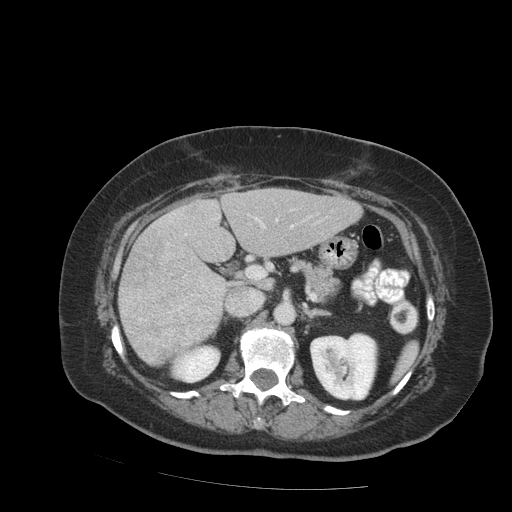
Contrast-enhanced abdominal CT (liver protocol), one axial slice. Slice 43 of 99 in the series (ordered by position). Soft-tissue window (W 400 / L 40 HU). 512 × 512 image matrix. Case-level facts recorded for this patient, not image findings: diagnosis: hepatocellular carcinoma (patient treated with transarterial chemoembolisation; whether this scan precedes or follows treatment is not stated here); TNM stage (as recorded): Stage-IVB; Child-Pugh class: A.
Structures marked on this image (semi-automatically segmented with operator editing):
- liver parenchyma outside the tumour (the mass and vessels are separate outlines, so this box may not span the whole liver): box from (x=118, y=188) to (x=362, y=364) px
- mass: (x=120, y=234)–(x=222, y=364)
- liver vessels: (x=170, y=209)–(x=311, y=236)